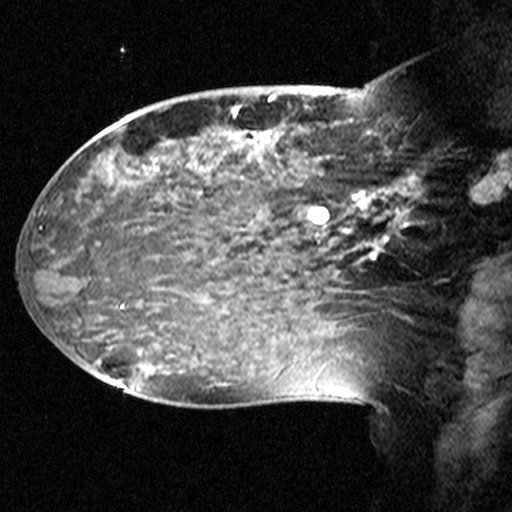
Breast MRI (dynamic contrast-enhanced), one sagittal slice; position 18 of 44 along the scan axis; dynamic contrast-enhanced study with each time point stored as its own series, time point 2 of 3 at this slice position (early post-contrast, ordered by acquisition time); 1.5 T; TE 4.5 ms, TR 11 ms; 3 mm slice thickness; 512 × 512 image matrix, field of view 240 × 240 mm. Patient: female, 38 years. From the clinical record (not read from this slice): setting: breast cancer imaged before/during neoadjuvant chemotherapy; receptor status: HR-positive, HER2-negative.
Structures marked on this image (semi-automatically segmented with operator editing):
- analysis volume of interest (the breast-tissue region the enhancement analysis was run in; not a lesion): bounding box (x1, y1, x2, y2) in pixels: (124, 106, 405, 245)
- tumour enhancement mask (voxels above the 90 % enhancement threshold inside the analysis volume of interest): (230, 106, 388, 243)